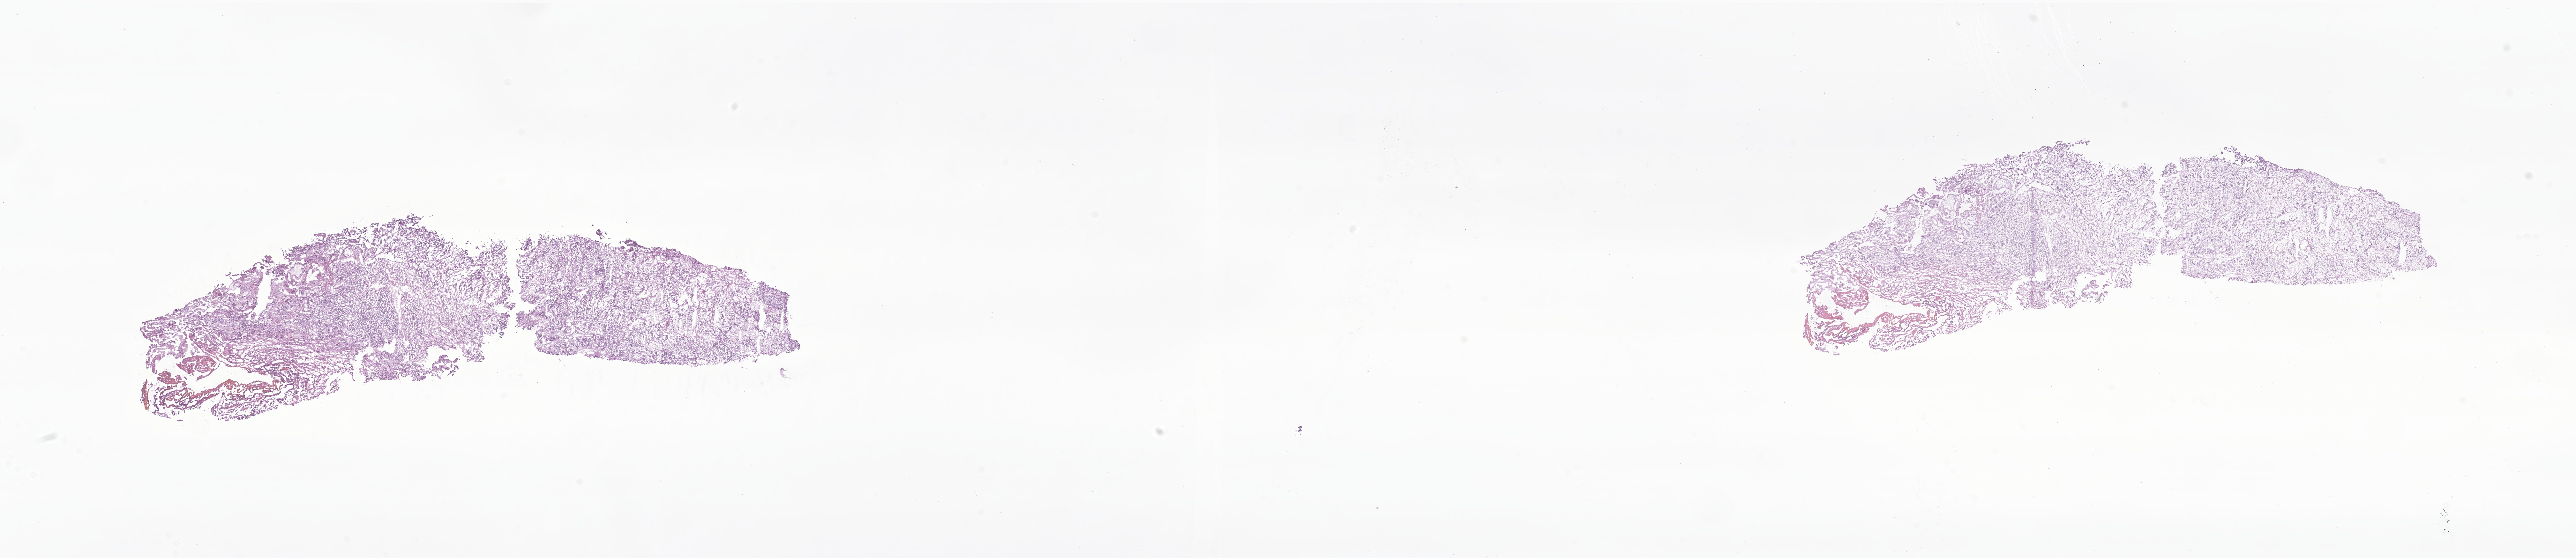
Hematoxylin and eosin (H&E) whole-slide image of tumor tissue from the brain, whole scanned area (about 34.0 x 7.4 mm) shown as a low-resolution overview. Cryosection (OCT / tissue freezing medium). Patient: male, age 138 months.
Diagnosis (ICD-O-3 morphology term): Ependymoma, NOS.